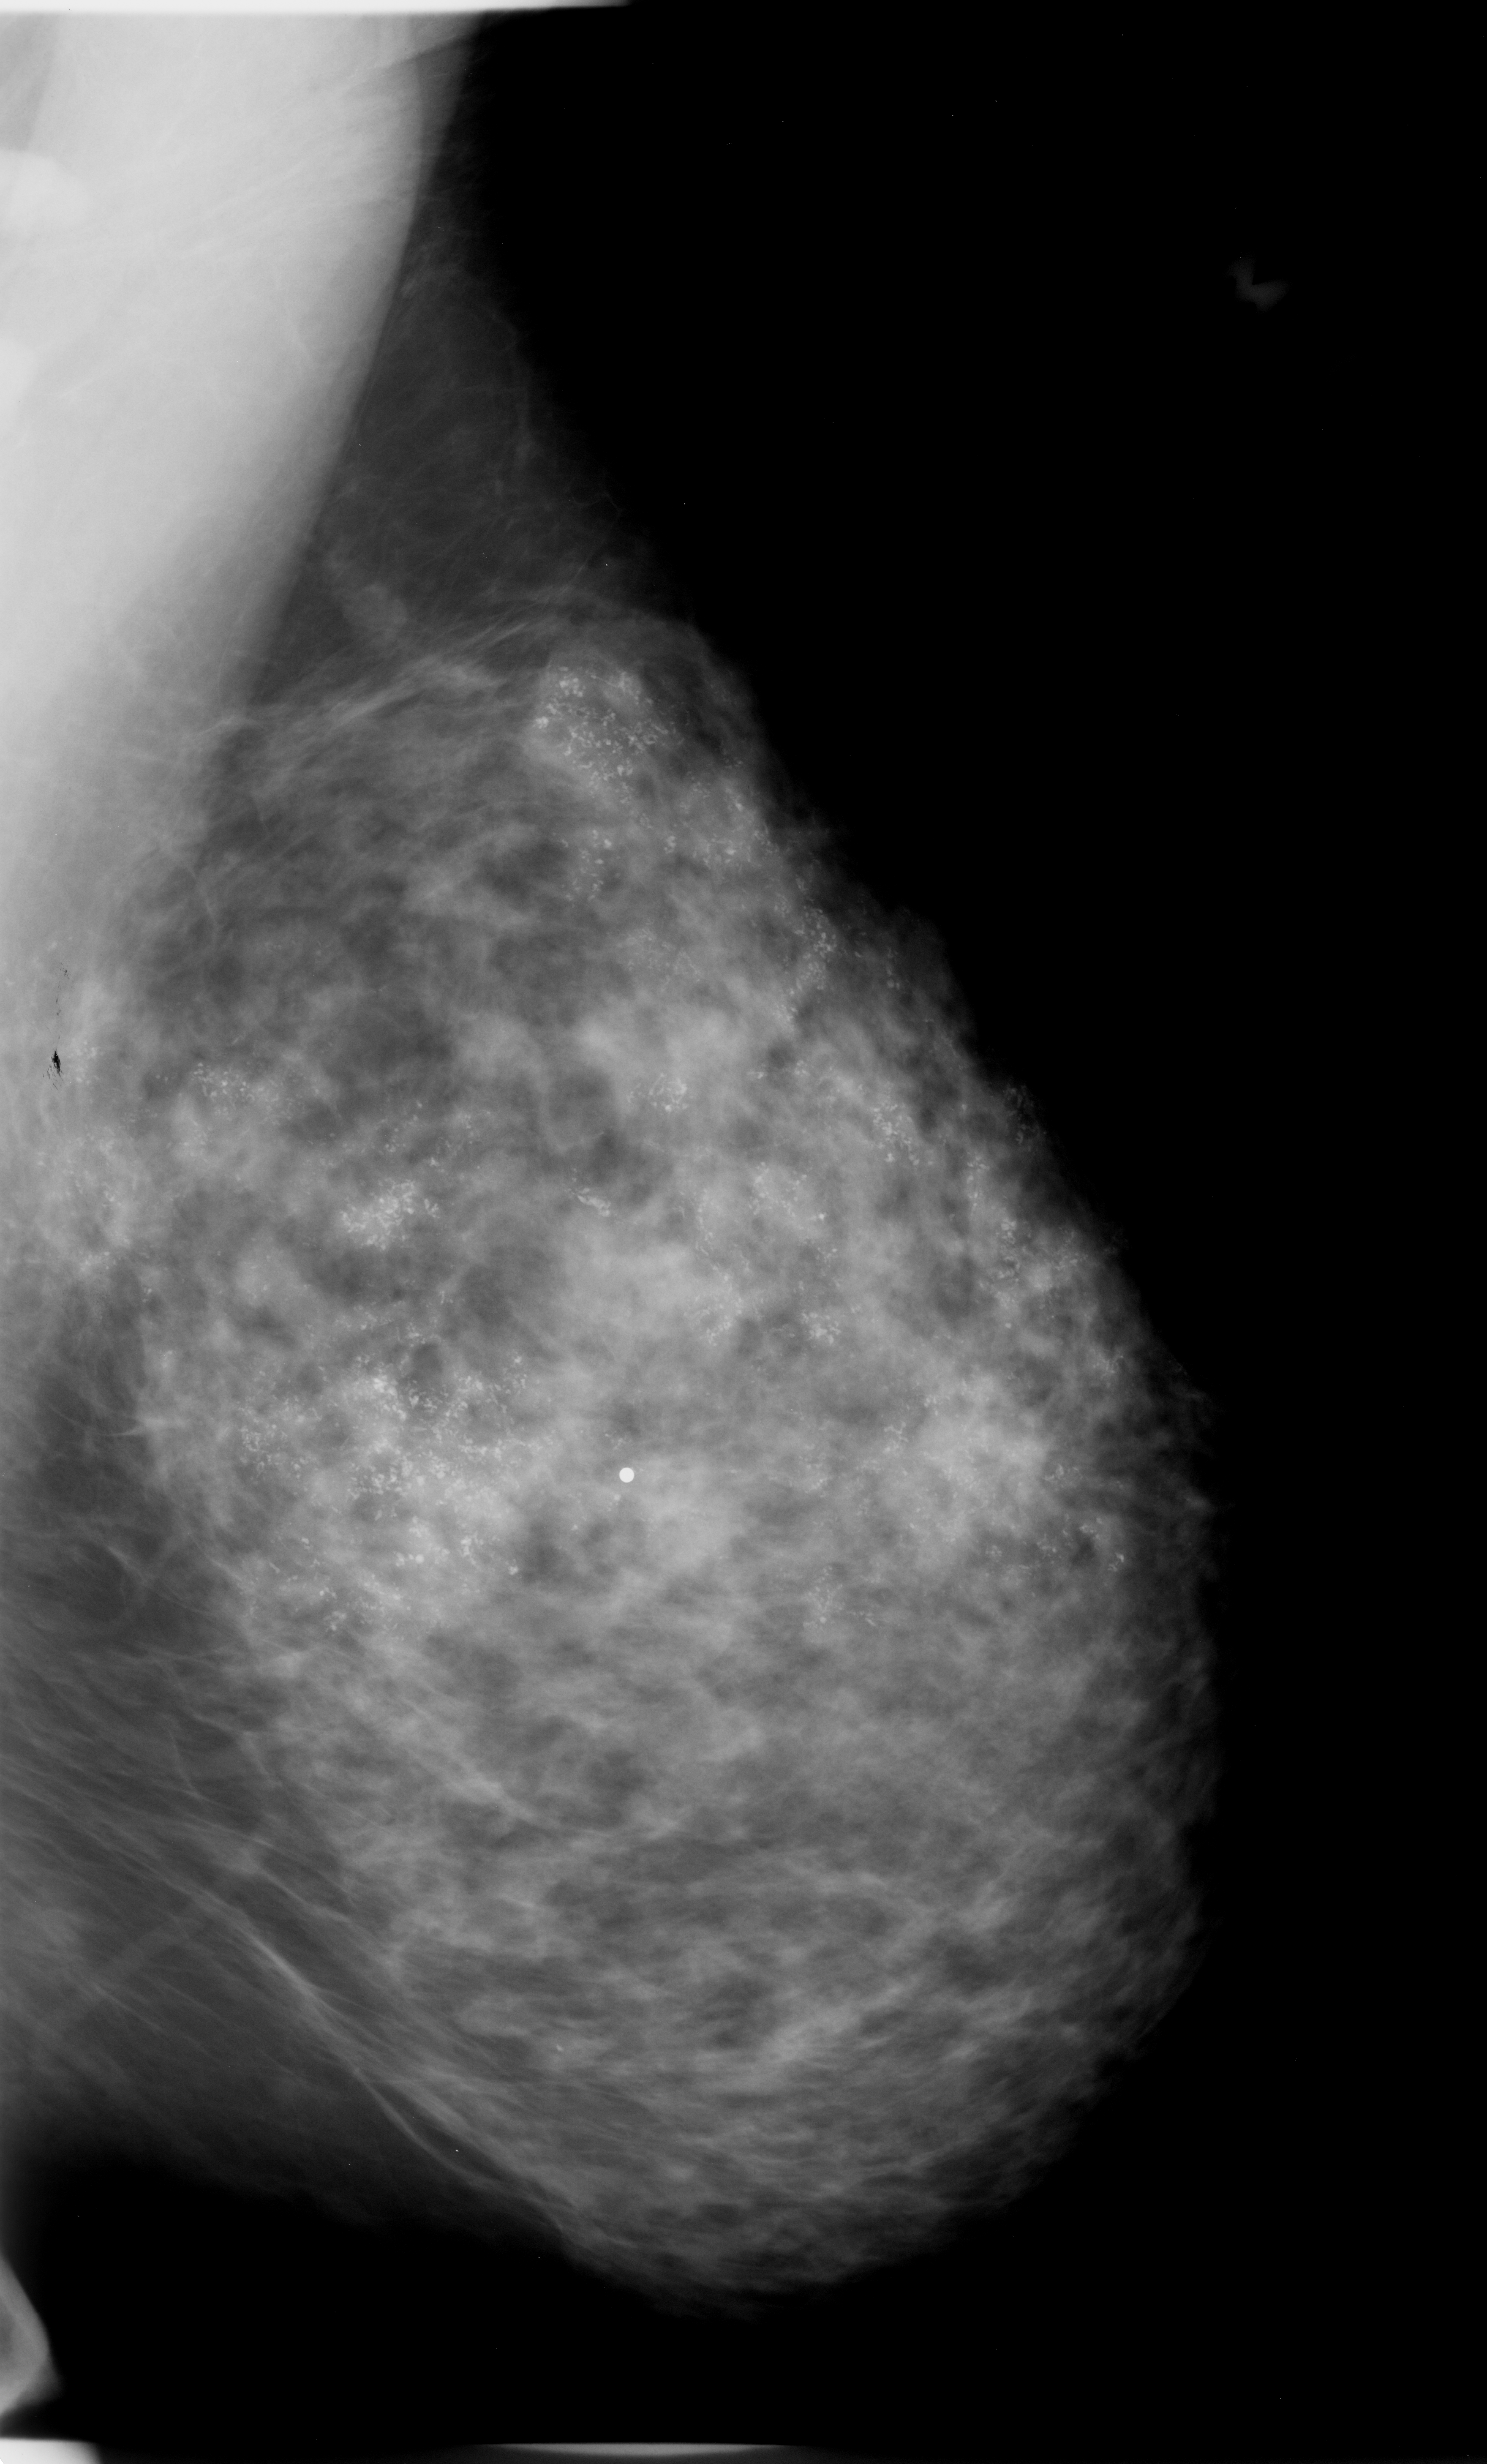
Mammogram (digitized film), left breast, mediolateral oblique (MLO) view, BI-RADS breast density category 3 (scale 1–4).
Calcifications, morphology pleomorphic, distribution regional; BI-RADS assessment category 5; subtlety rating 5 on a 1 (subtle) to 5 (obvious) scale; pathology (as recorded): malignant.